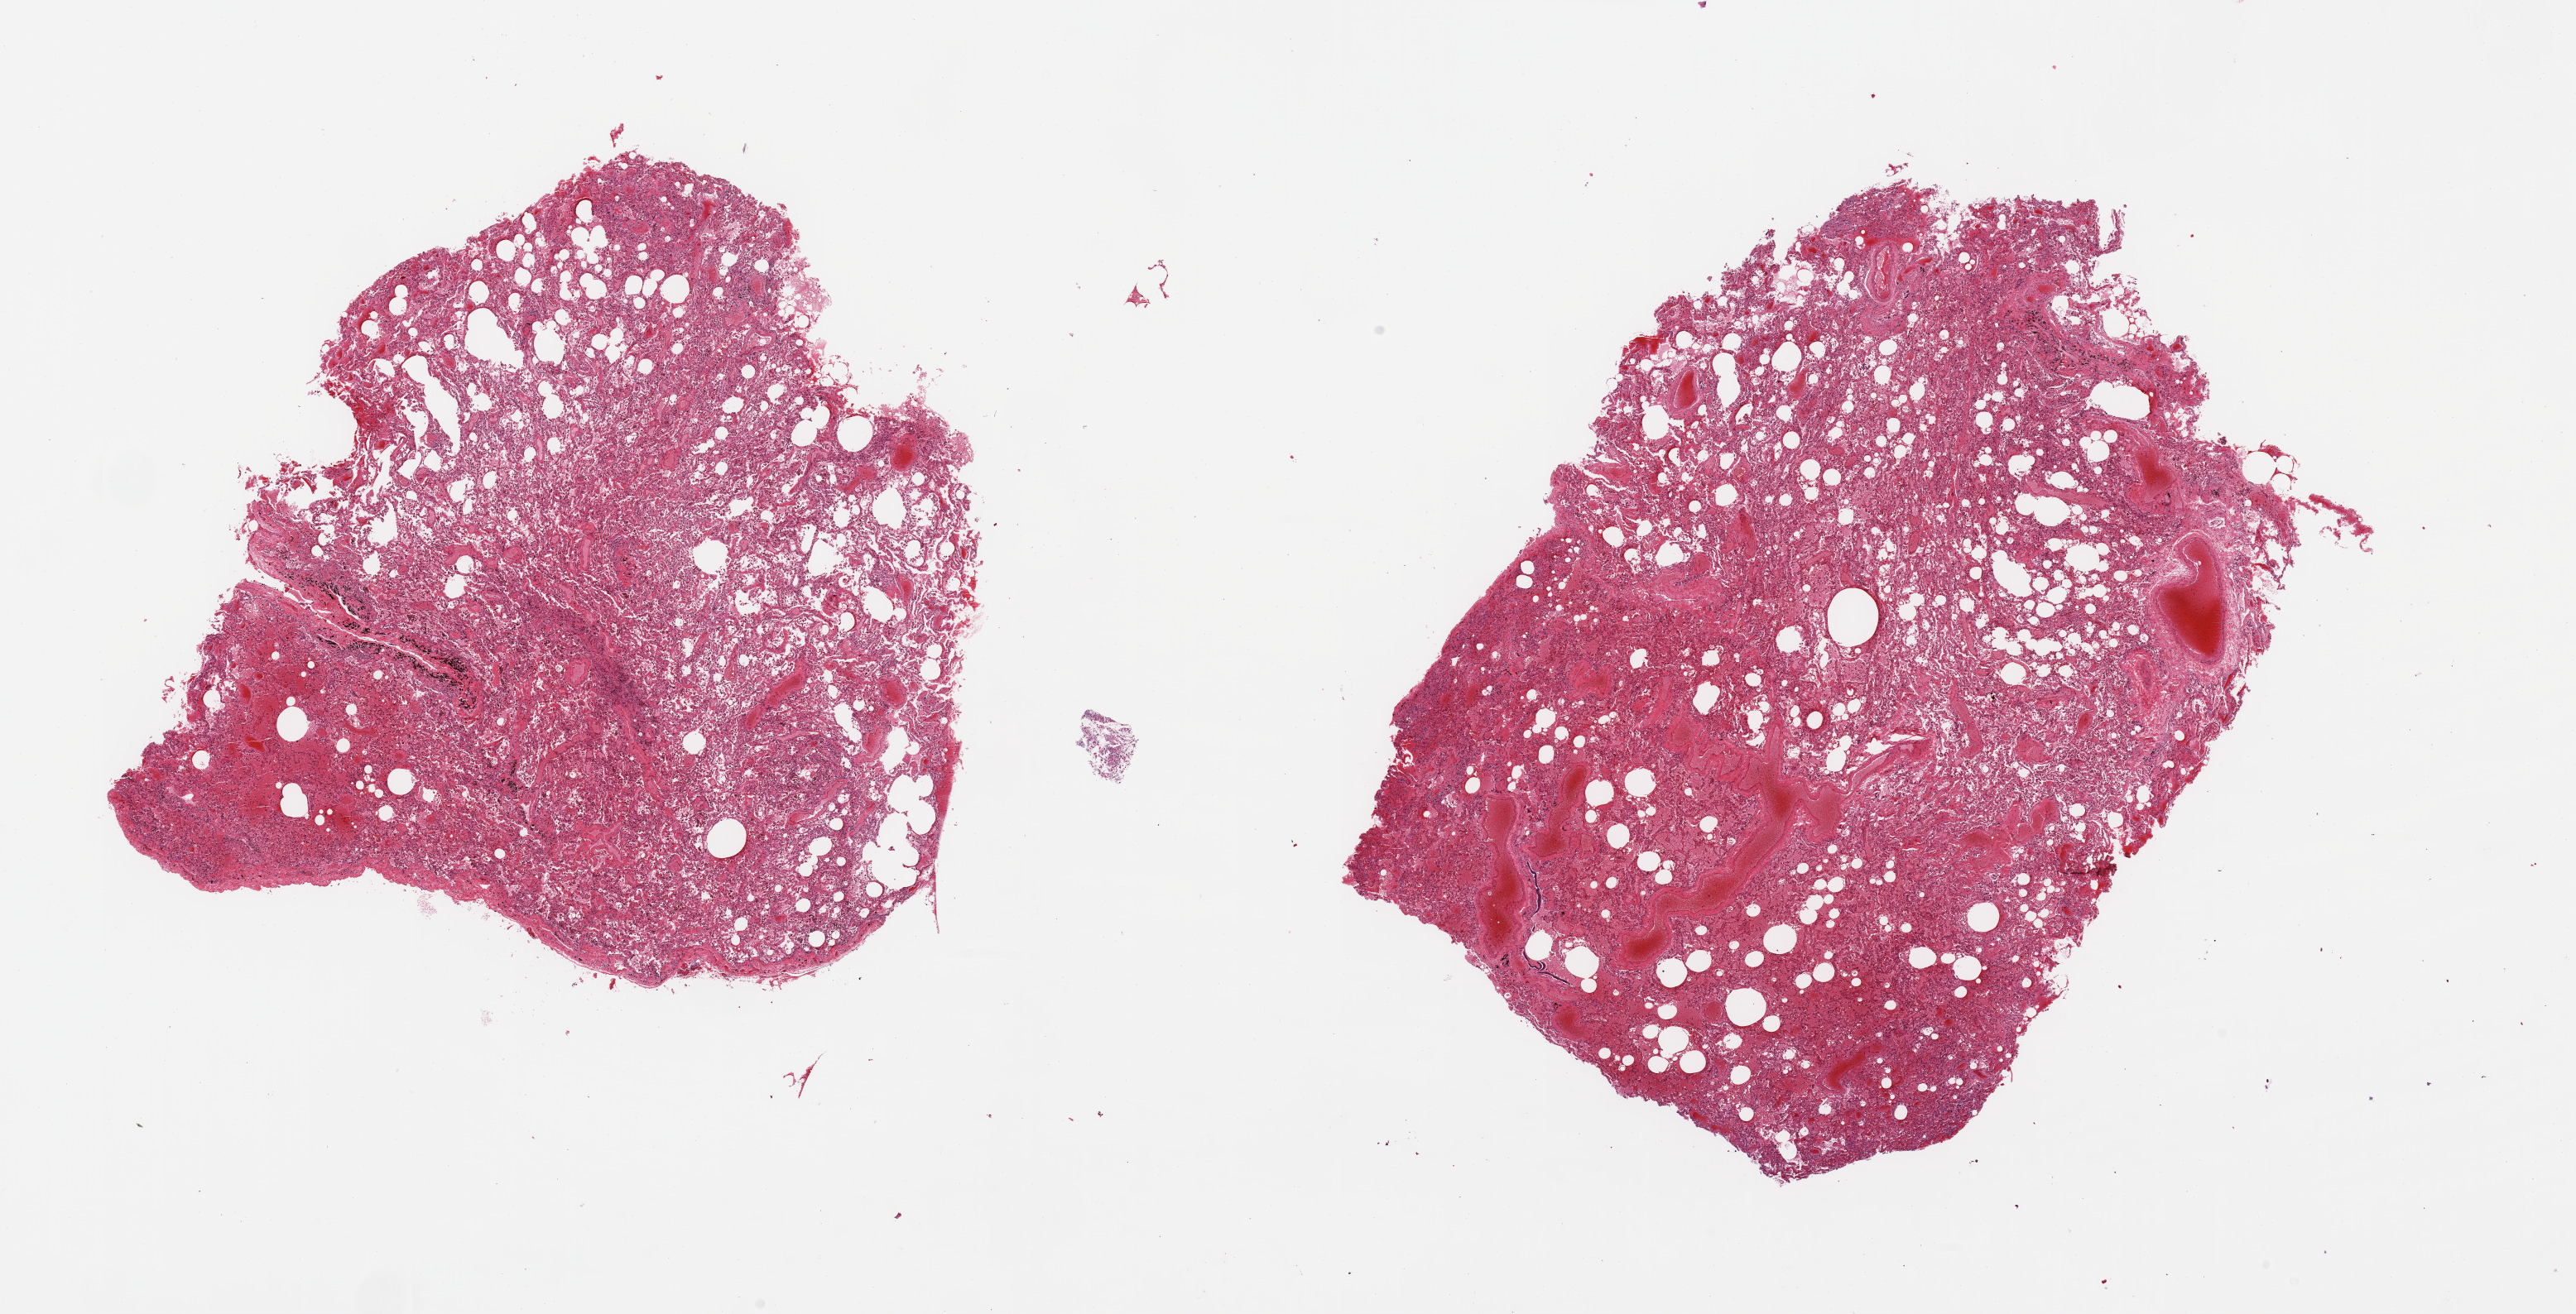
Whole-slide image, H&E stain — whole scanned area (about 24.6 x 12.6 mm, slide scanned at 20x) shown as a low-resolution overview. PAXgene-fixed paraffin-embedded (PFPE) section. Section of lung (target tissue). Tissue donor sample. Donor: male.
• review note (as recorded): 2 pieces; moderate vascular congestion, alveolar hemorrhages and pigmented macrophages